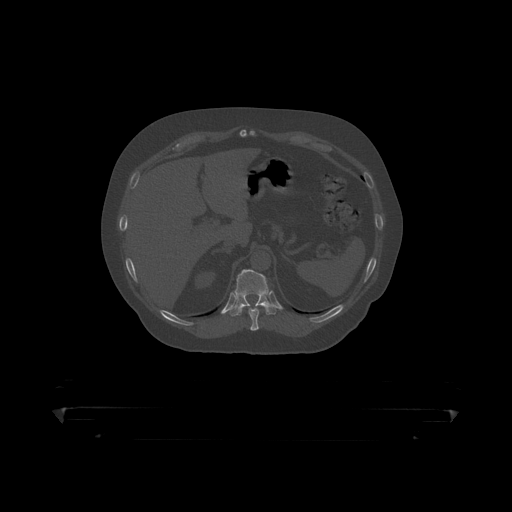
CT including the spine, one axial slice. Slice 202 of 390 in the series (ordered by position). Bone window (W 1800 / L 400 HU). 1.25 mm slice thickness. 512 × 512 image matrix, field of view 650 × 650 mm. Male patient, age 60 years. From the clinical record (not read from this slice): primary cancer: prostate.
Outlined on this slice (semi-automatic segmentation, software-assisted and operator-edited):
- T10 vertebra: bounding box <243,304,262,319> (left, top, right, bottom; pixels)
- T11 vertebra: <228,270,279,316>